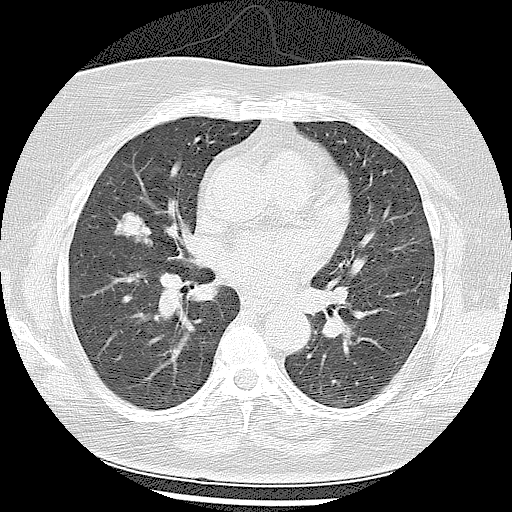
Low-dose screening chest CT, one axial slice; position 51 of 102 along the scan axis; lung window (W 1500 / L -600 HU); 2.5 mm slice thickness; 512 × 512 image matrix, field of view 350 × 350 mm.
Annotated regions visible in this slice (manually delineated by an expert):
- lesion 1 (tumor, middle lobe of right lung): bounding box <114,212,153,246> (left, top, right, bottom; pixels)